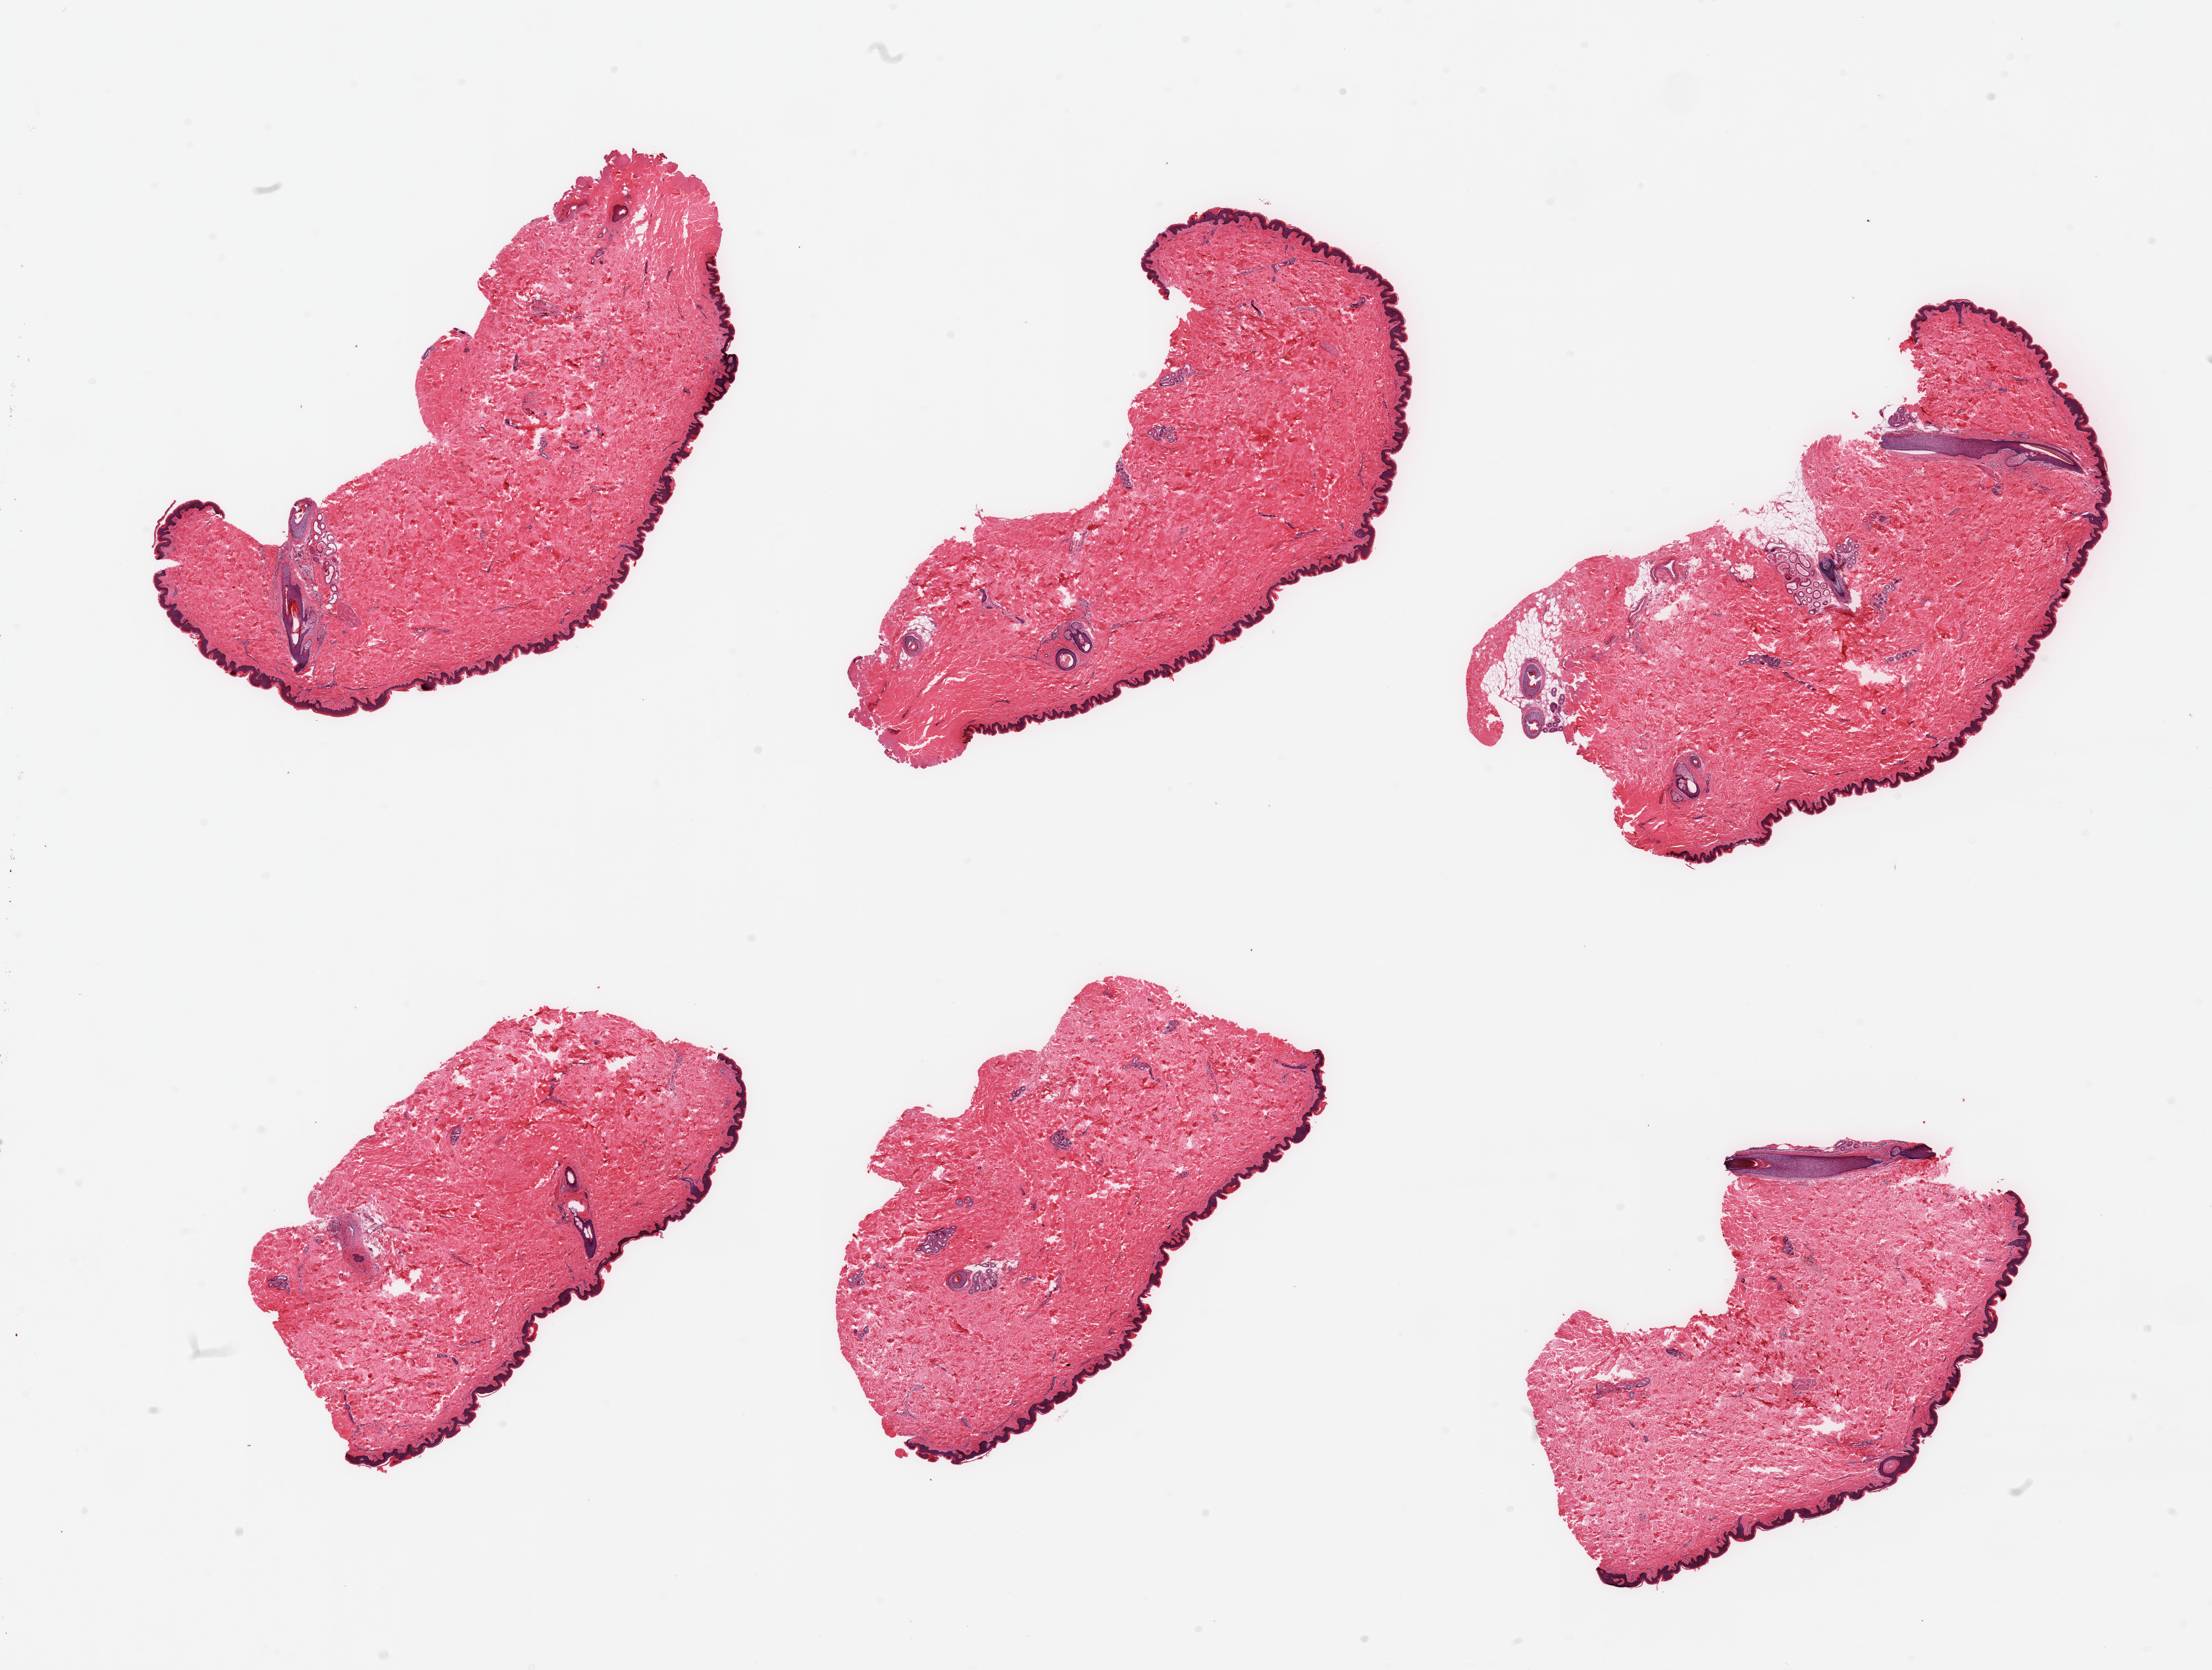
Whole-slide image, H&E stain — whole scanned area (about 26.6 x 20.1 mm, from a 20x scan) shown as a low-resolution overview; PAXgene-fixed paraffin-embedded (PFPE) section; section of skin of suprapubic region (target tissue); donor tissue sample.
* reviewer comment on this tissue sample: 6 pieces; hair bearing skin with trace of periadnexal fat